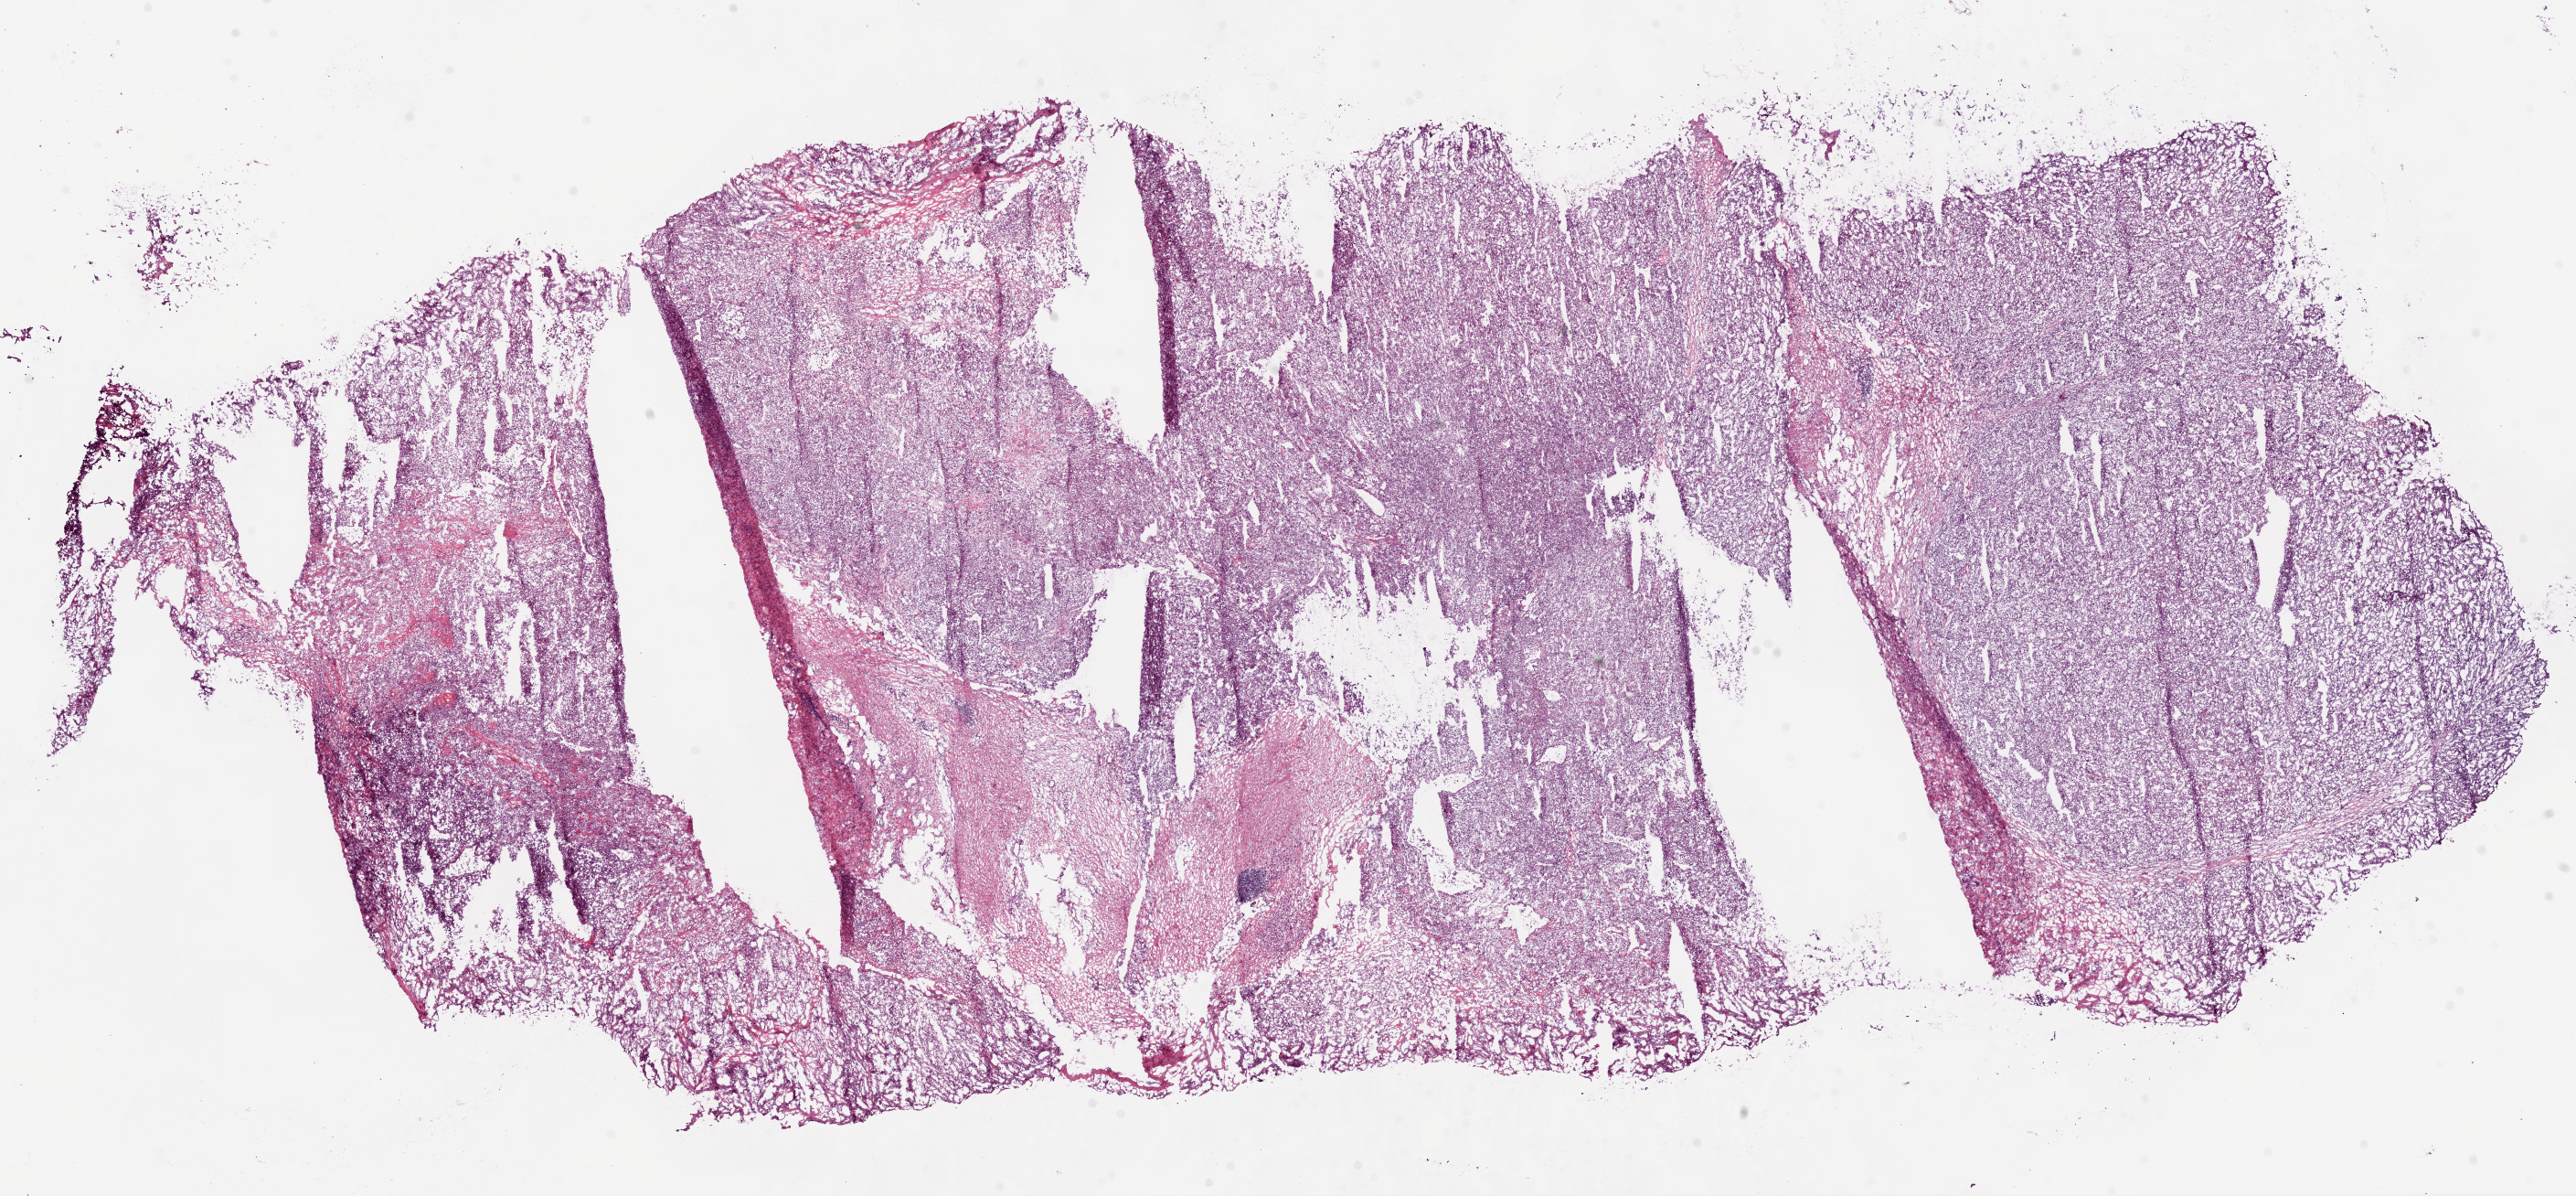
Digitized H&E tissue section (whole slide) — whole scanned area (about 22.7 x 10.5 mm) shown as a low-resolution overview; frozen section; kidney, primary tumour sample. Patient: female, age at initial diagnosis 54 years. Histologic grade: G4 (undifferentiated). Composition of this section per pathologist review: tumour cells 80%, tumour nuclei 80%, normal cells 0%, stromal cells 20%, necrosis 0%. Infiltration values recorded for this section: lymphocyte infiltration 5%, monocyte infiltration 0%, neutrophil infiltration 0%.
AJCC pathologic stage: IV. Histologic diagnosis: Clear cell adenocarcinoma, NOS.